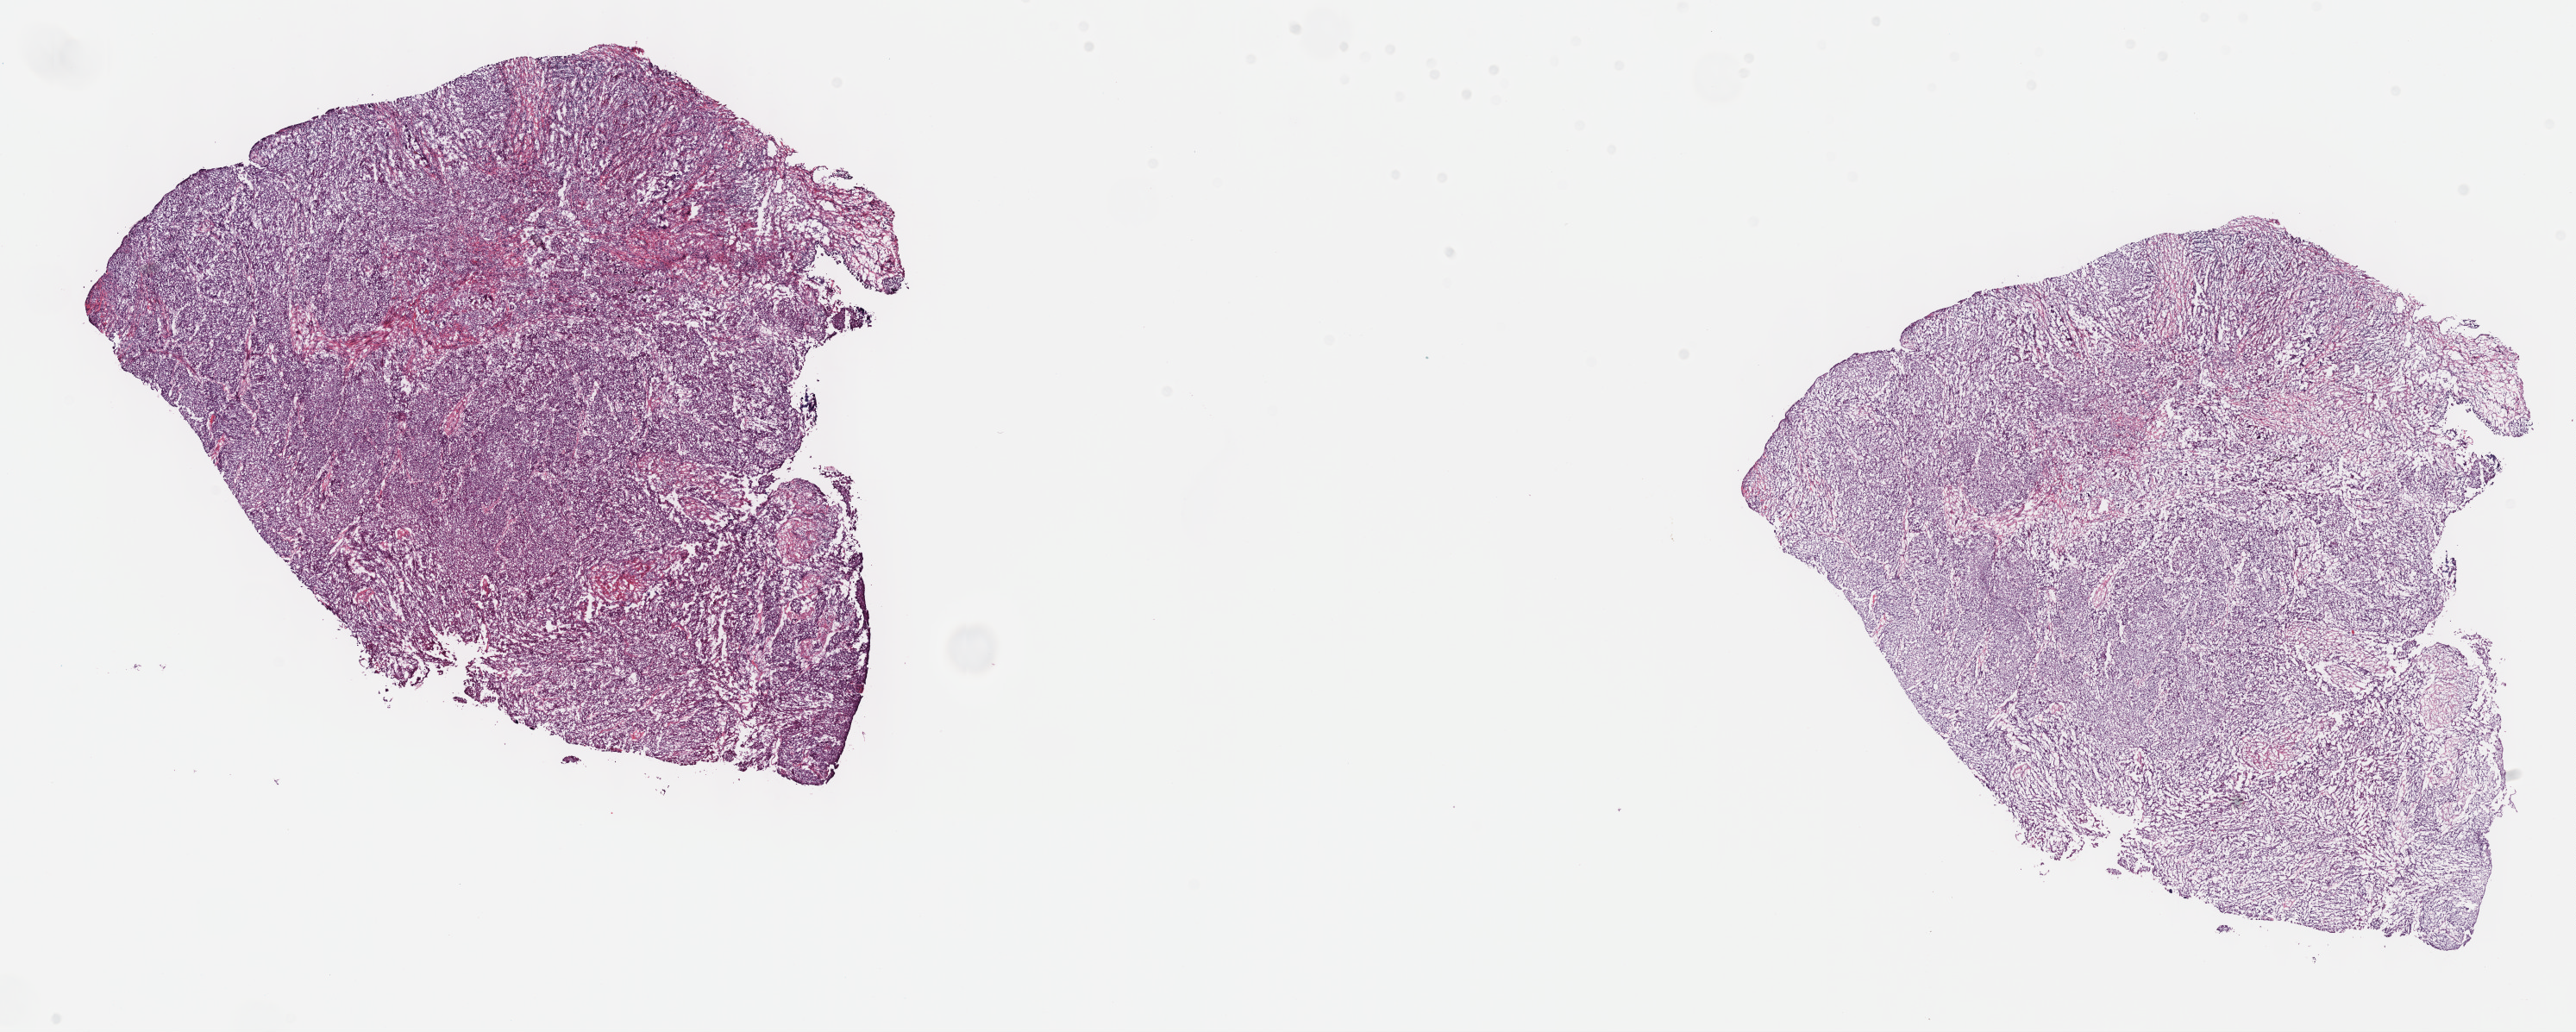
Whole-slide histology image, H&E-stained — shown as a low-resolution overview of the whole scanned area (about 24.2 x 9.7 mm, slide scanned at 40x), frozen section from the top of the tissue portion, bladder, primary tumour sample. Patient: female, age at initial diagnosis 78 years. Histologic grade: high grade. Pathologist review of this section (percent, as recorded): tumour cells 75%, tumour nuclei 75%, normal cells 0%, stromal cells 23%, necrosis 2%. Infiltration values recorded for this section: lymphocyte infiltration 3%, monocyte infiltration 1%, neutrophil infiltration 5%.
- pathologic diagnosis: Transitional cell carcinoma
- AJCC pathologic stage: II (6th edition)